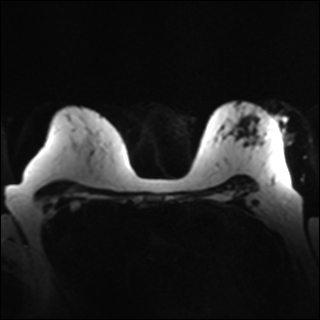
Breast MRI, one axial slice; slice 20 of 35 in the series (ordered by position); diffusion-weighted series; image 2 of 4 stored at this slice position (different b-values; order by instance number); 1.5 T; 320 × 320 image matrix, field of view 320 × 320 mm. Female patient.
Annotated regions visible in this slice (manually delineated by an expert):
- tumour on diffusion-weighted imaging: box from (x=268, y=120) to (x=278, y=136) px